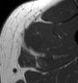
MRI of an extremity soft-tissue mass, one axial slice; position 33 of 43 along the scan axis; MR volume resampled by the dataset authors to the PET/CT grid (not the native acquisition matrix); 3.27 mm slice thickness; 78 × 83 image matrix, field of view 76 × 81 mm. Male patient. Case-level facts recorded for this patient, not image findings: histological type: pleiomorphic leiomyosarcoma; grade: high; site of the primary tumour: left thigh.
Outlined on this slice (expert contour drawn on MRI and transferred to this co-registered scan by the dataset authors):
- gross tumour volume including surrounding oedema: bounding box [x1, y1, x2, y2] px = [20, 28, 42, 57]